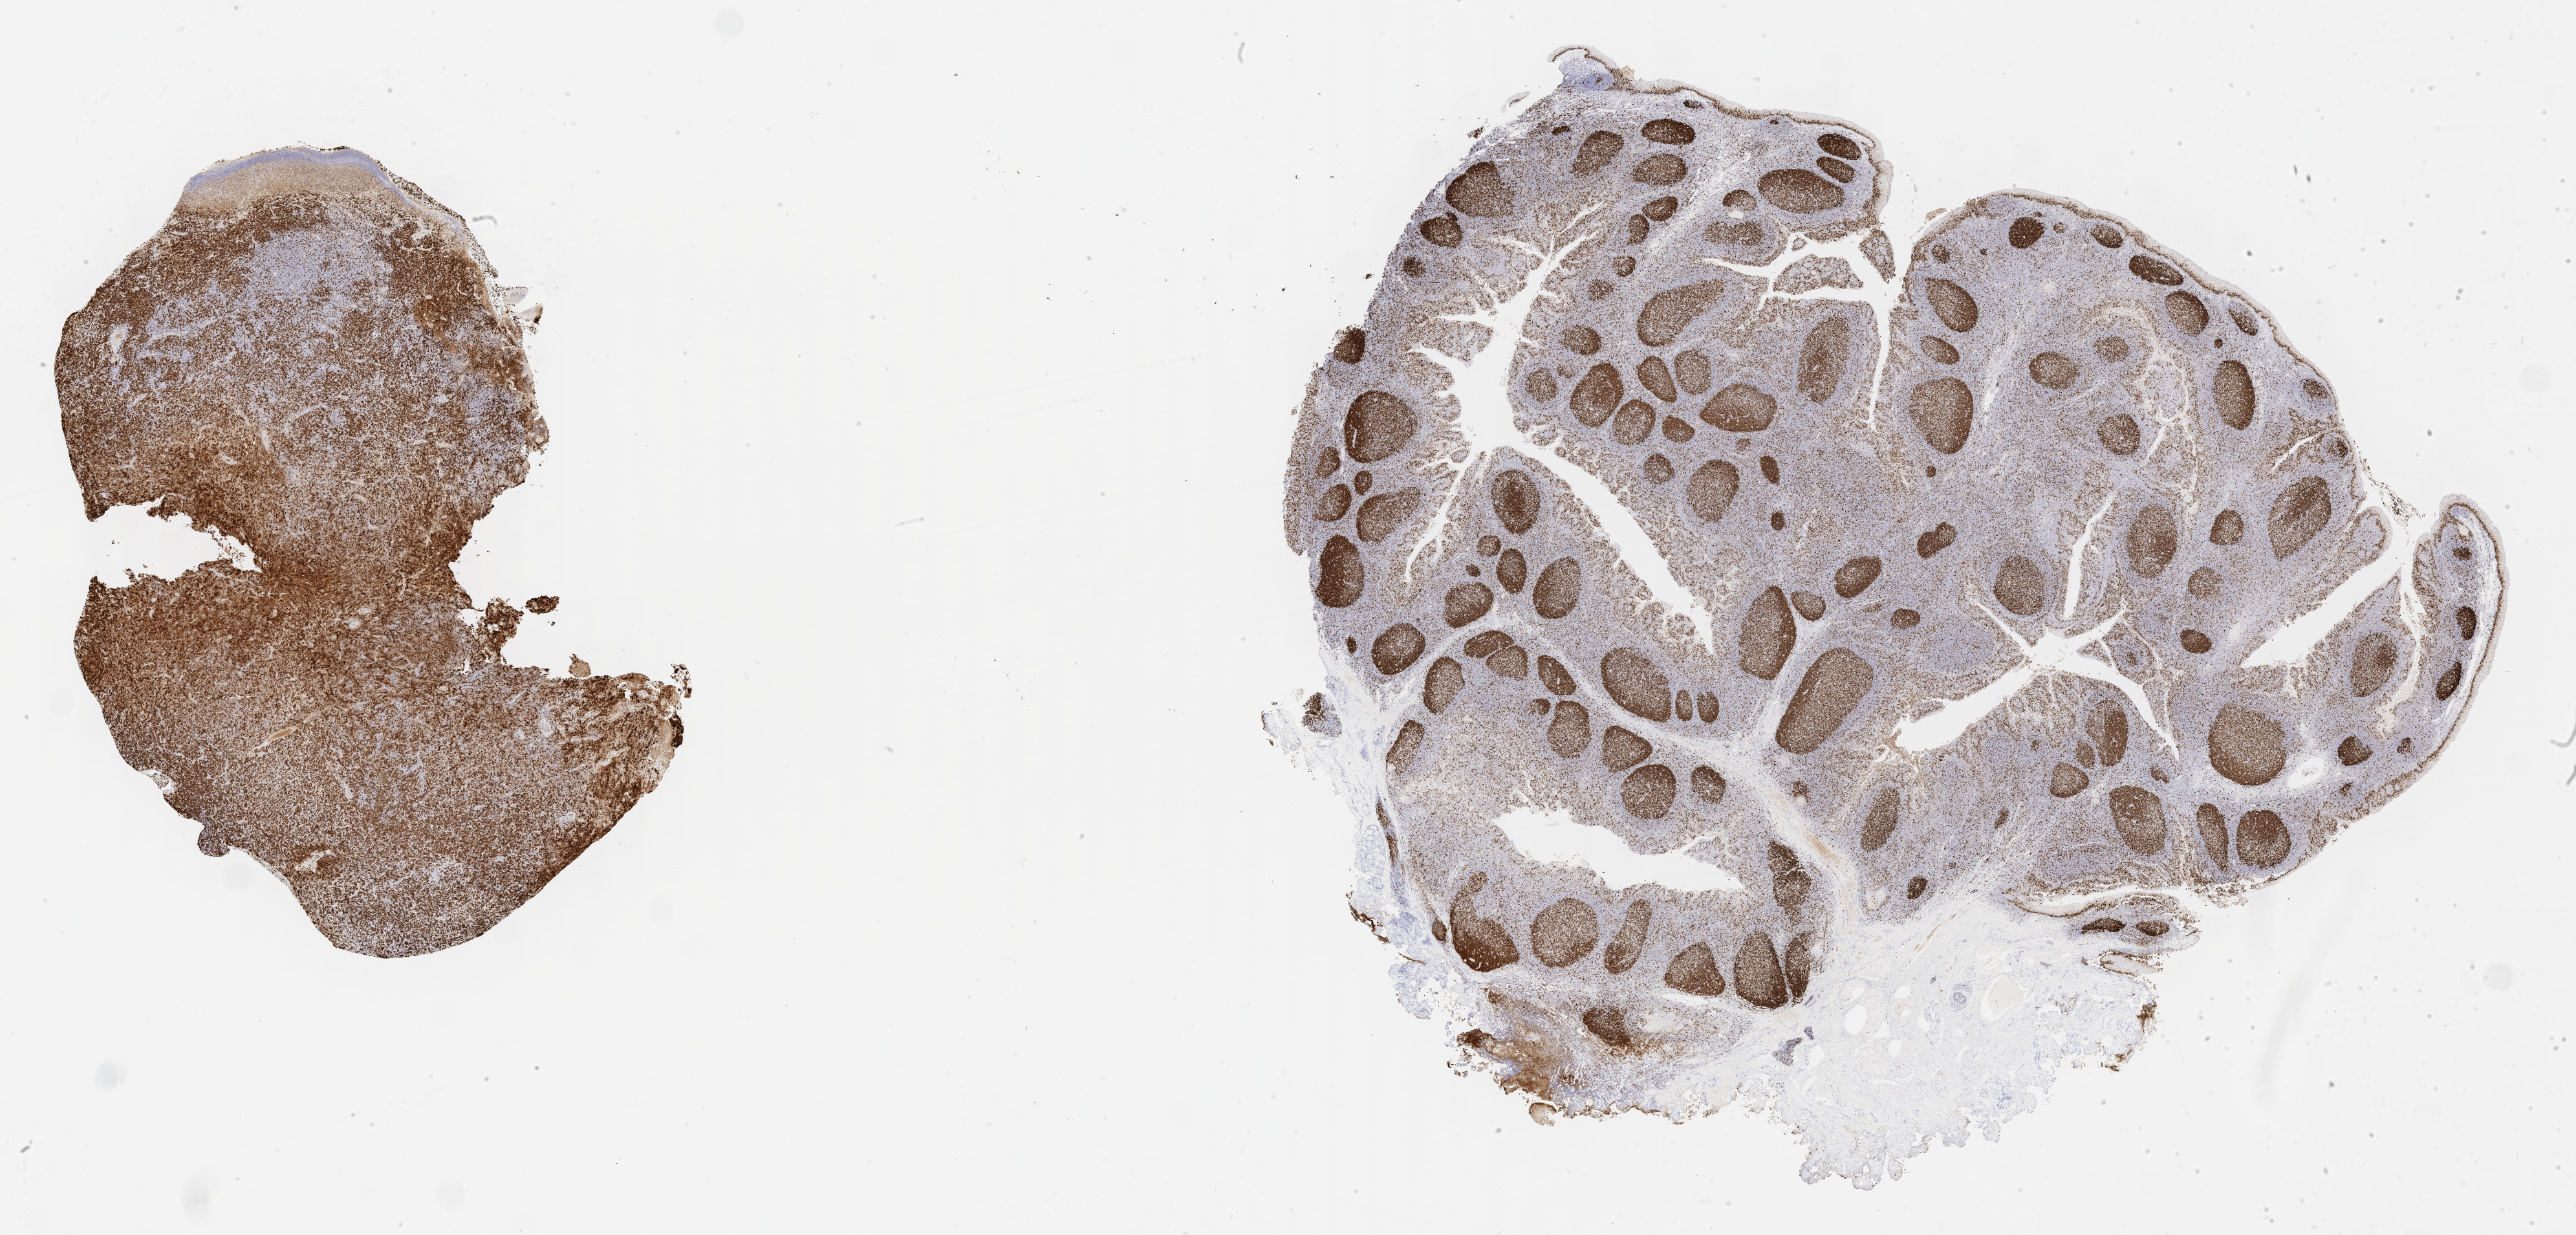
Immunohistochemistry (IHC) whole-slide image stained for Ki-67, low-resolution overview of the scanned area, about 32.2 x 15.4 mm, specimen: tumor tissue. Patient: male, age at initial diagnosis 7 years.
• histologic diagnosis: Diffuse large B-cell lymphoma, NOS